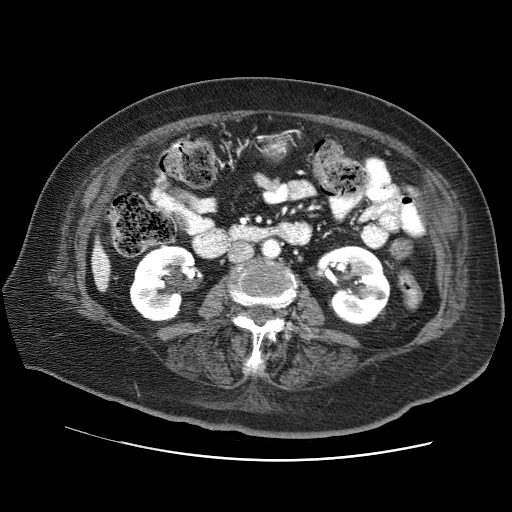
Contrast-enhanced abdominal CT (liver protocol), one axial slice; slice 15 of 73 in the series (ordered by position); soft-tissue window (W 400 / L 40 HU); 2.5 mm slice thickness; 512 × 512 image matrix, field of view 380 × 380 mm. From the clinical record (not read from this slice): diagnosis: hepatocellular carcinoma (patient treated with transarterial chemoembolisation; whether this scan precedes or follows treatment is not stated here); TNM stage (as recorded): Stage-I; Child-Pugh class: A; tumour nodularity: uninodular.
Structures marked on this image (semi-automatic segmentation, software-assisted and operator-edited):
- liver parenchyma outside the tumour (the mass and vessels are separate outlines, so this box may not span the whole liver): bounding box (x1, y1, x2, y2) in pixels: (92, 240, 110, 290)
- liver vessels: (95, 250, 106, 275)